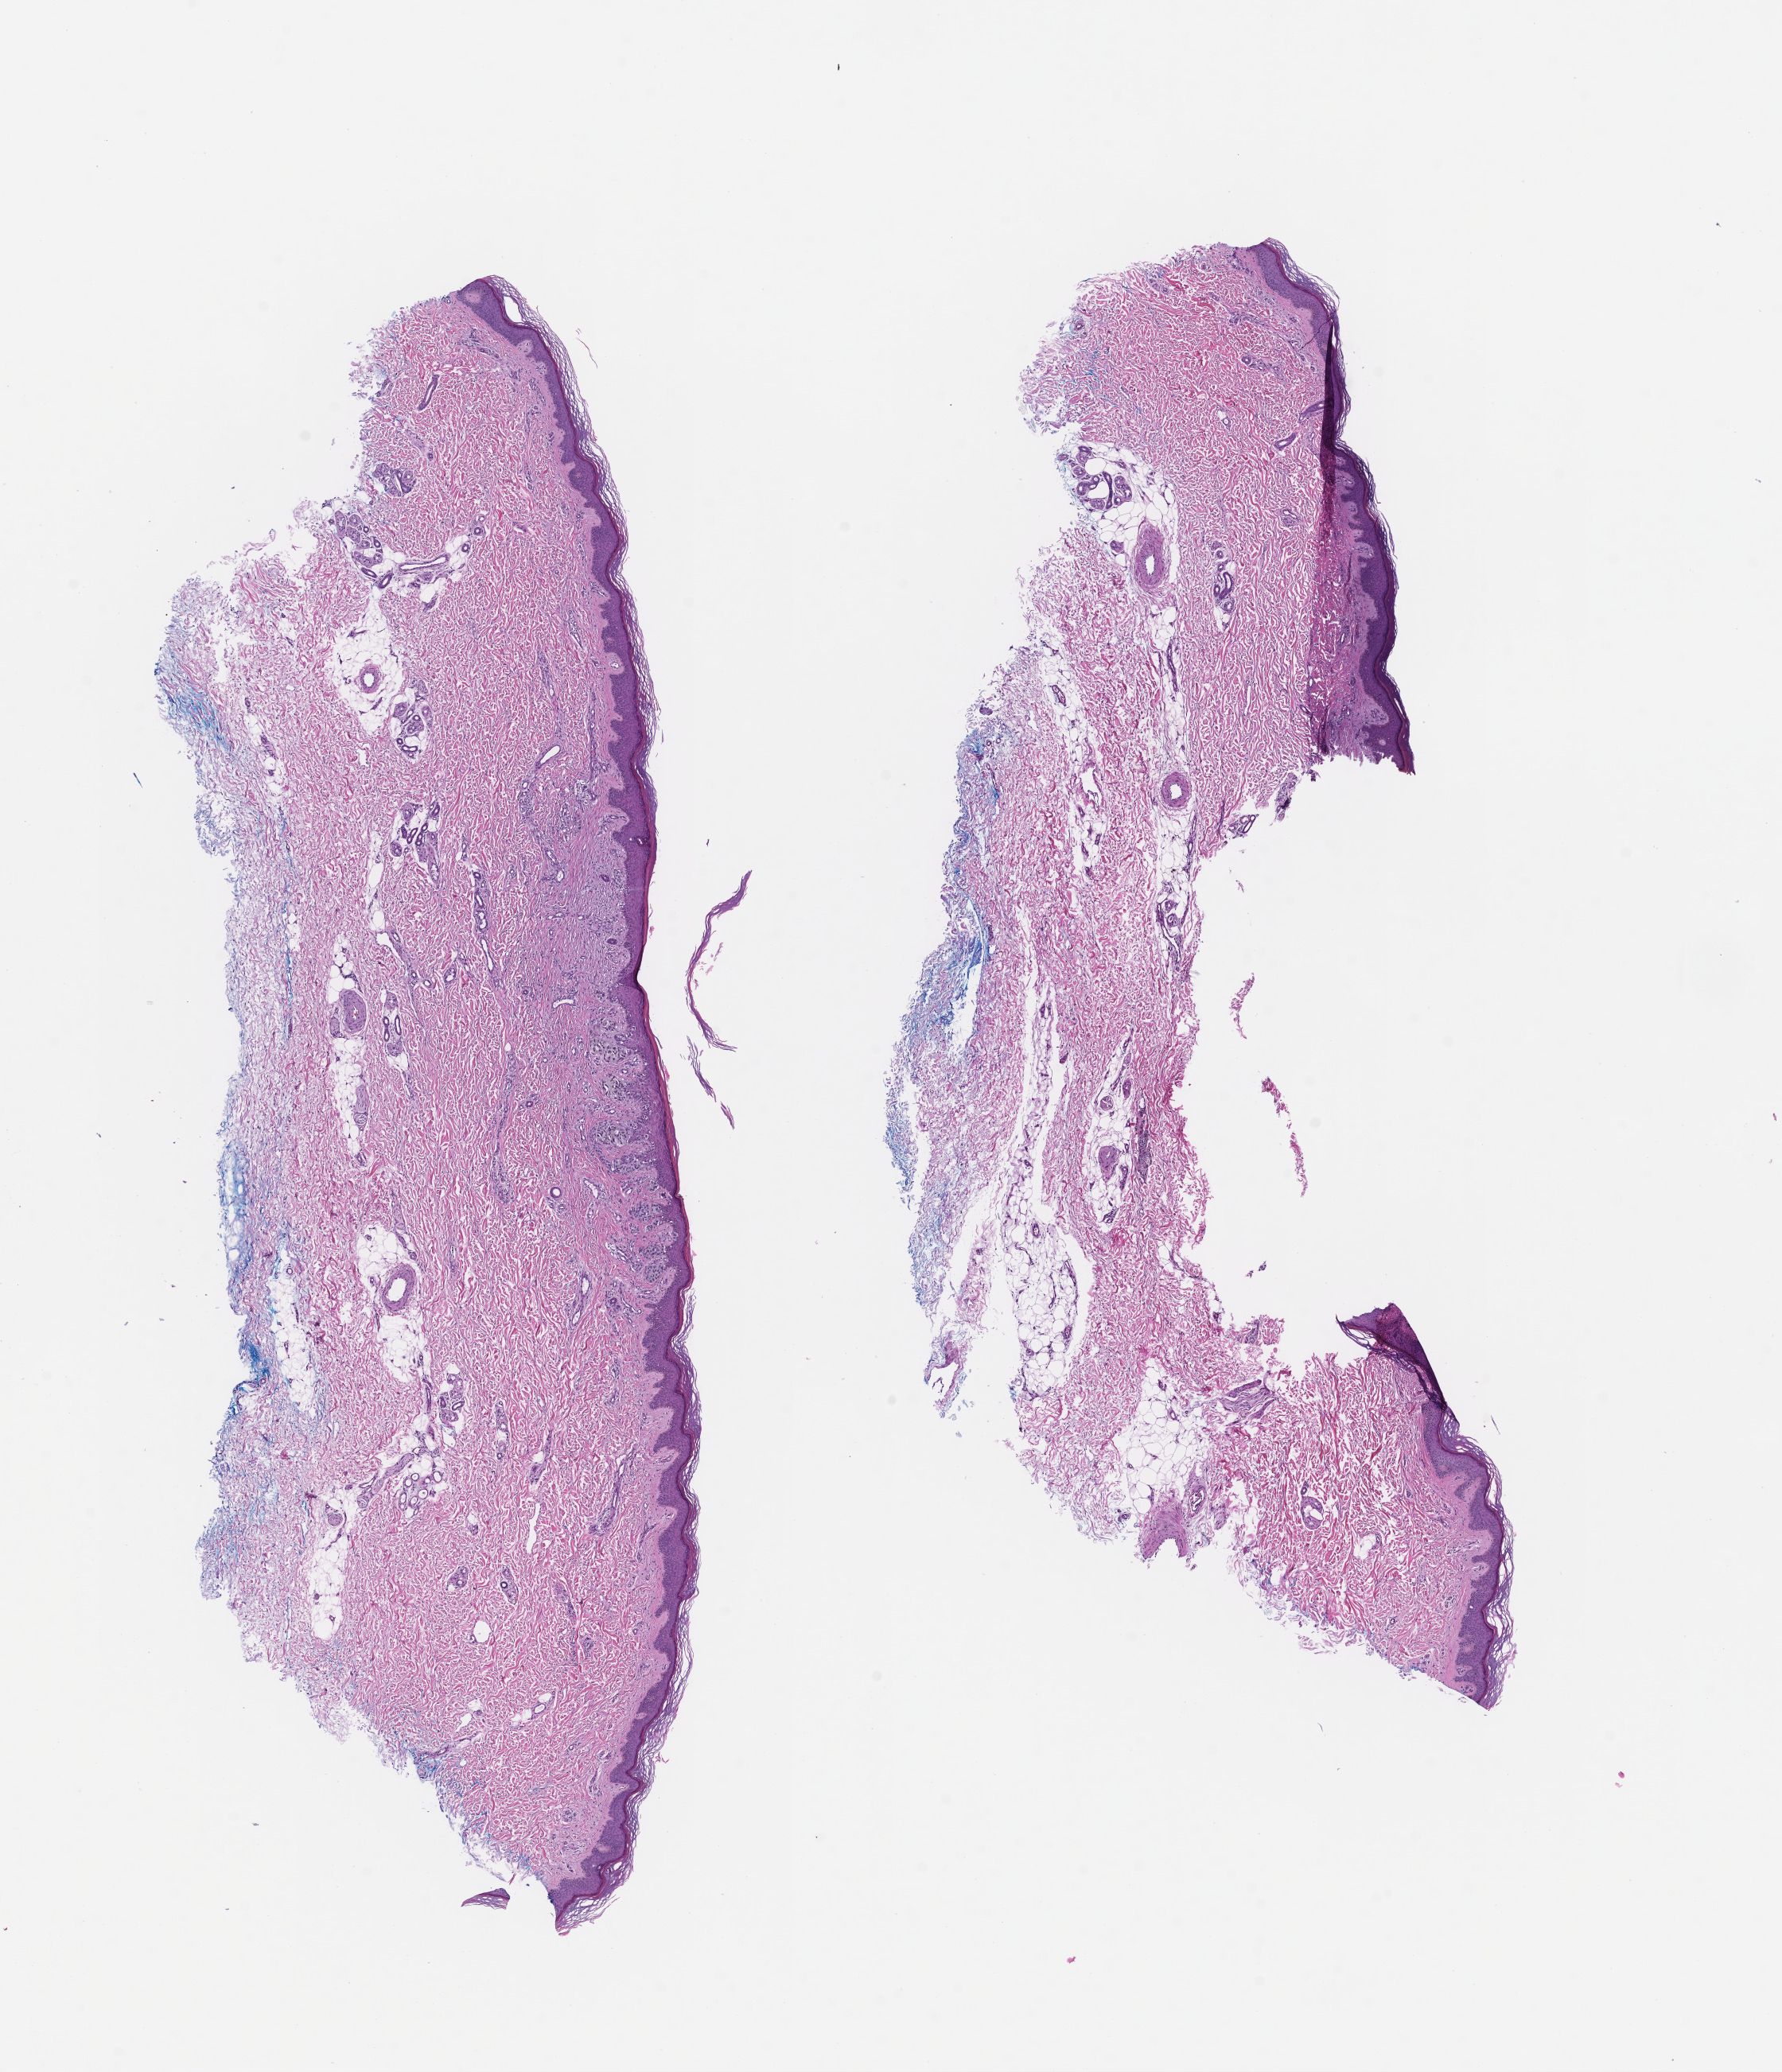
Hematoxylin and eosin (H&E) whole-slide image, a low-resolution overview of the entire scanned area, about 9.0 x 10.5 mm. Formalin-fixed, paraffin-embedded (FFPE) tissue. Tissue site: skin. Specimen time point: archival tissue. Patient sex: female.
This section: primary tumour tissue. Diagnosis: Melanoma.